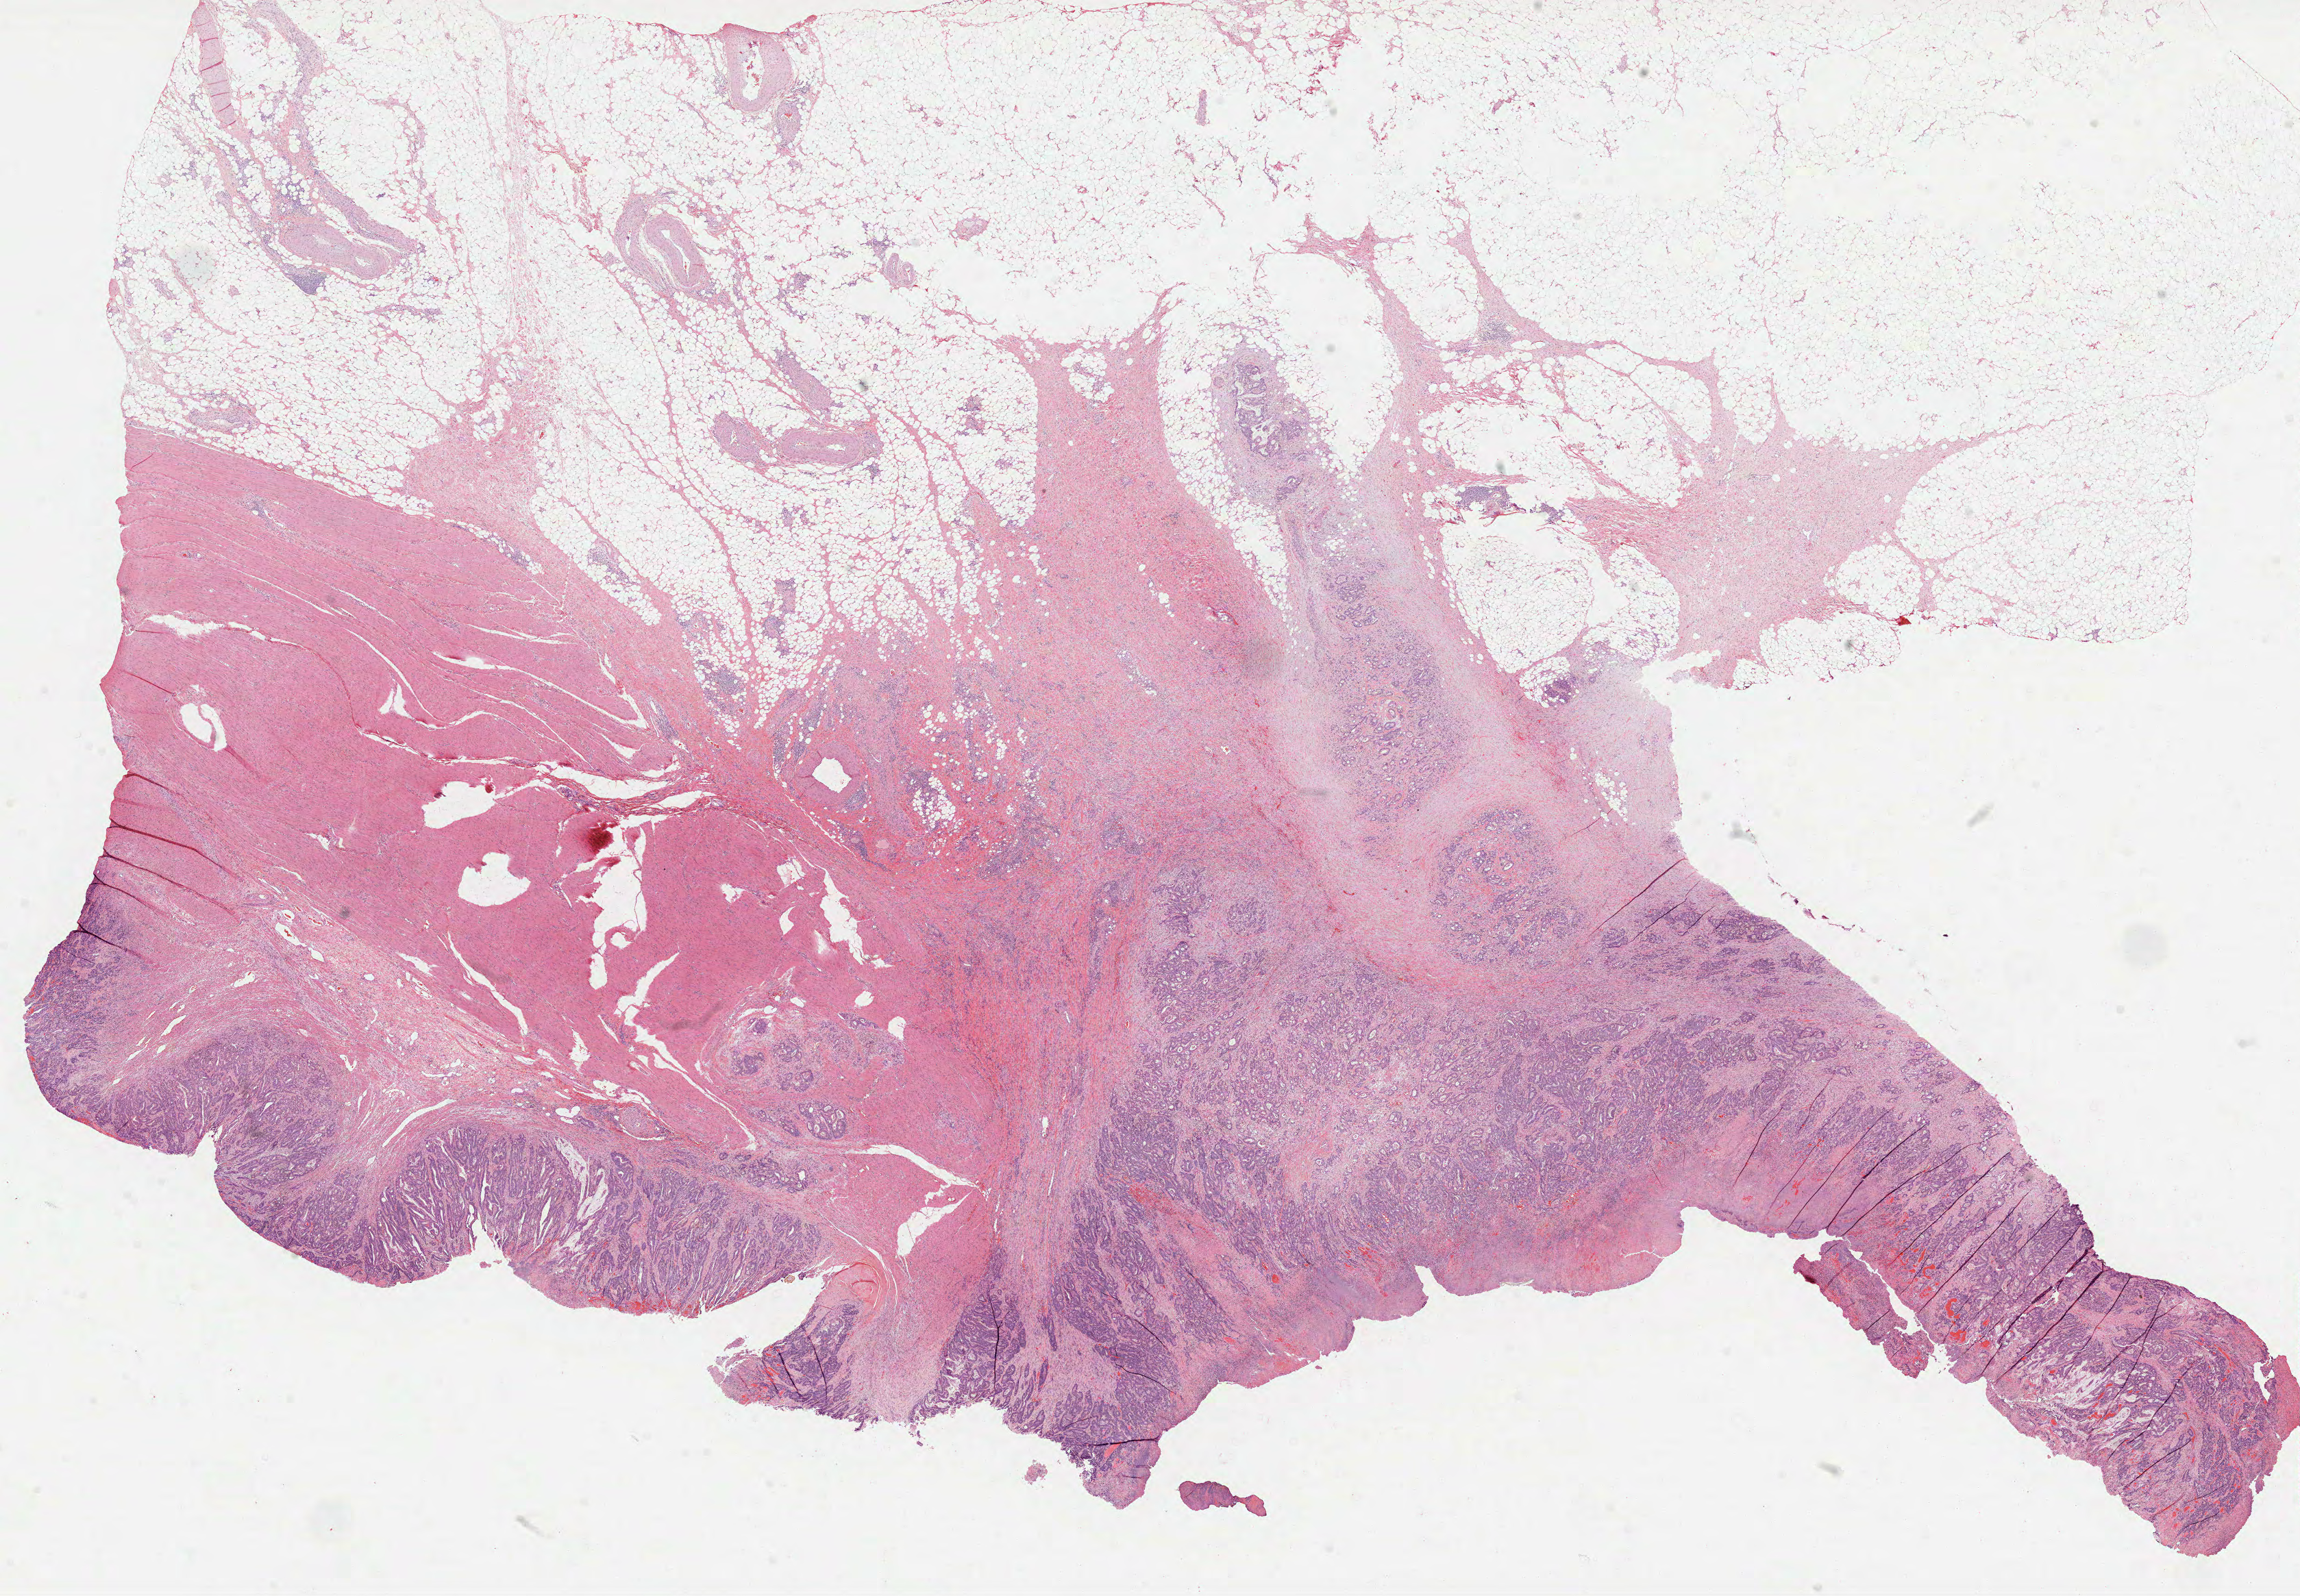
Digitized H&E-stained tissue section (whole slide), low-resolution overview of the scanned area, about 27.1 x 18.8 mm. Formalin-fixed paraffin-embedded (FFPE) diagnostic section. Rectum, primary tumour sample. Male, age 74 years at initial diagnosis.
Pathologic diagnosis: Adenocarcinoma, NOS. Lymph nodes positive (case pathology): 27 of 72 examined.